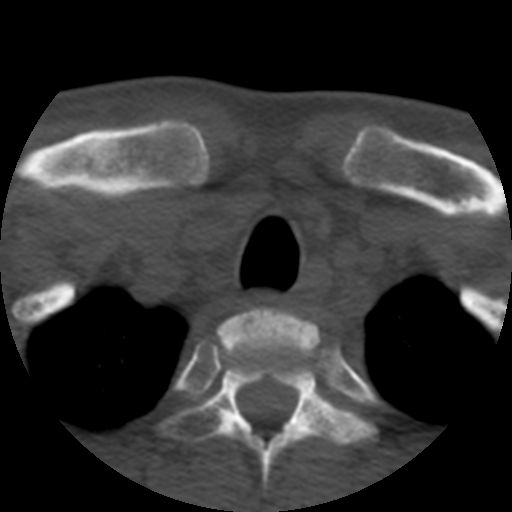
CT including the spine, one axial slice. Slice 436 of 508 in the series (ordered by position). Reconstruction kernel STANDARD. 120 kVp. Bone window (W 1800 / L 400 HU). 512 × 512 image matrix, field of view 160 × 160 mm. Patient age 57 years. From the clinical record (not read from this slice): primary cancer: prostate.
Annotated regions visible in this slice (semi-automatically segmented with operator editing):
- T1 vertebra: bounding box (x1, y1, x2, y2) in pixels: (217, 307, 320, 356)
- T2 vertebra: (154, 346, 377, 488)